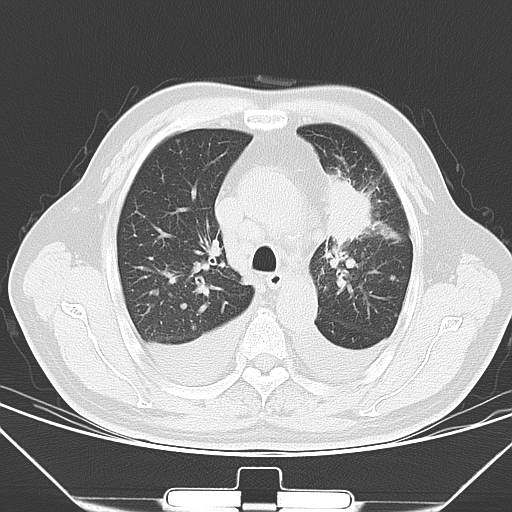
Chest CT, one axial slice. Position 45 of 66 along the scan axis. 120 kVp. Lung window (W 1500 / L -600 HU). 512 × 512 image matrix, field of view 352 × 352 mm. Male patient, age 66 years. Case-level facts recorded for this patient, not image findings: clinical TNM (as recorded): T1c N0 M0.
Outlined on this slice (rectangle marked by the reading radiologist):
- lung tumour (recorded histology: adenocarcinoma): box from (x=325, y=171) to (x=378, y=242) px